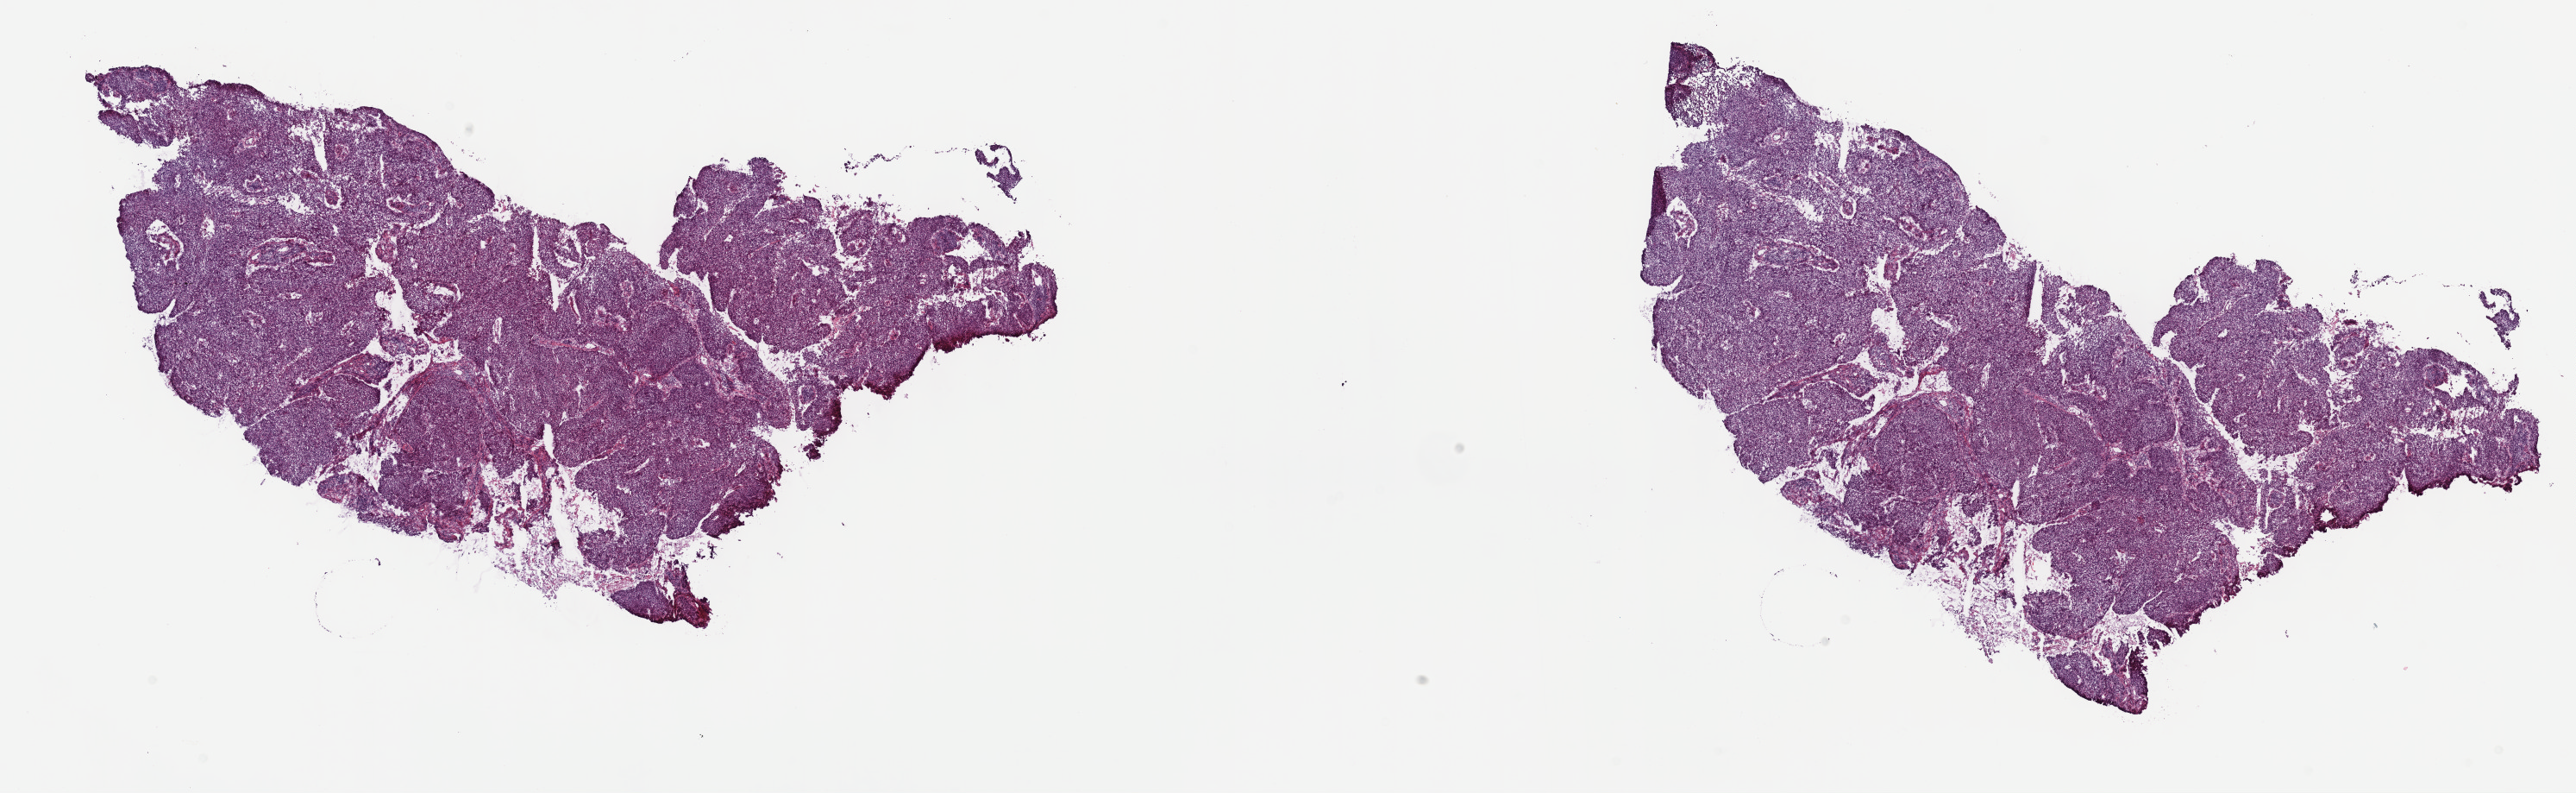
Whole-slide histology image, Hematoxylin and eosin (H&E) stained — whole scanned area (about 24.2 x 7.4 mm, from a 40x scan) shown as a low-resolution overview. Frozen section. Sample: primary tumour, cervix. Patient: female, age at initial diagnosis 30 years. Histologic grade: G3 (poorly differentiated). Slide review estimates, as recorded: tumour cells 90%, tumour nuclei 90%, normal cells 5%, stromal cells 5%, necrosis 0%. Inflammatory infiltration, as recorded: lymphocyte infiltration 5%, monocyte infiltration 0%, neutrophil infiltration 0%.
FIGO stage: IB1. Diagnosis: Squamous cell carcinoma, NOS (cervix uteri).